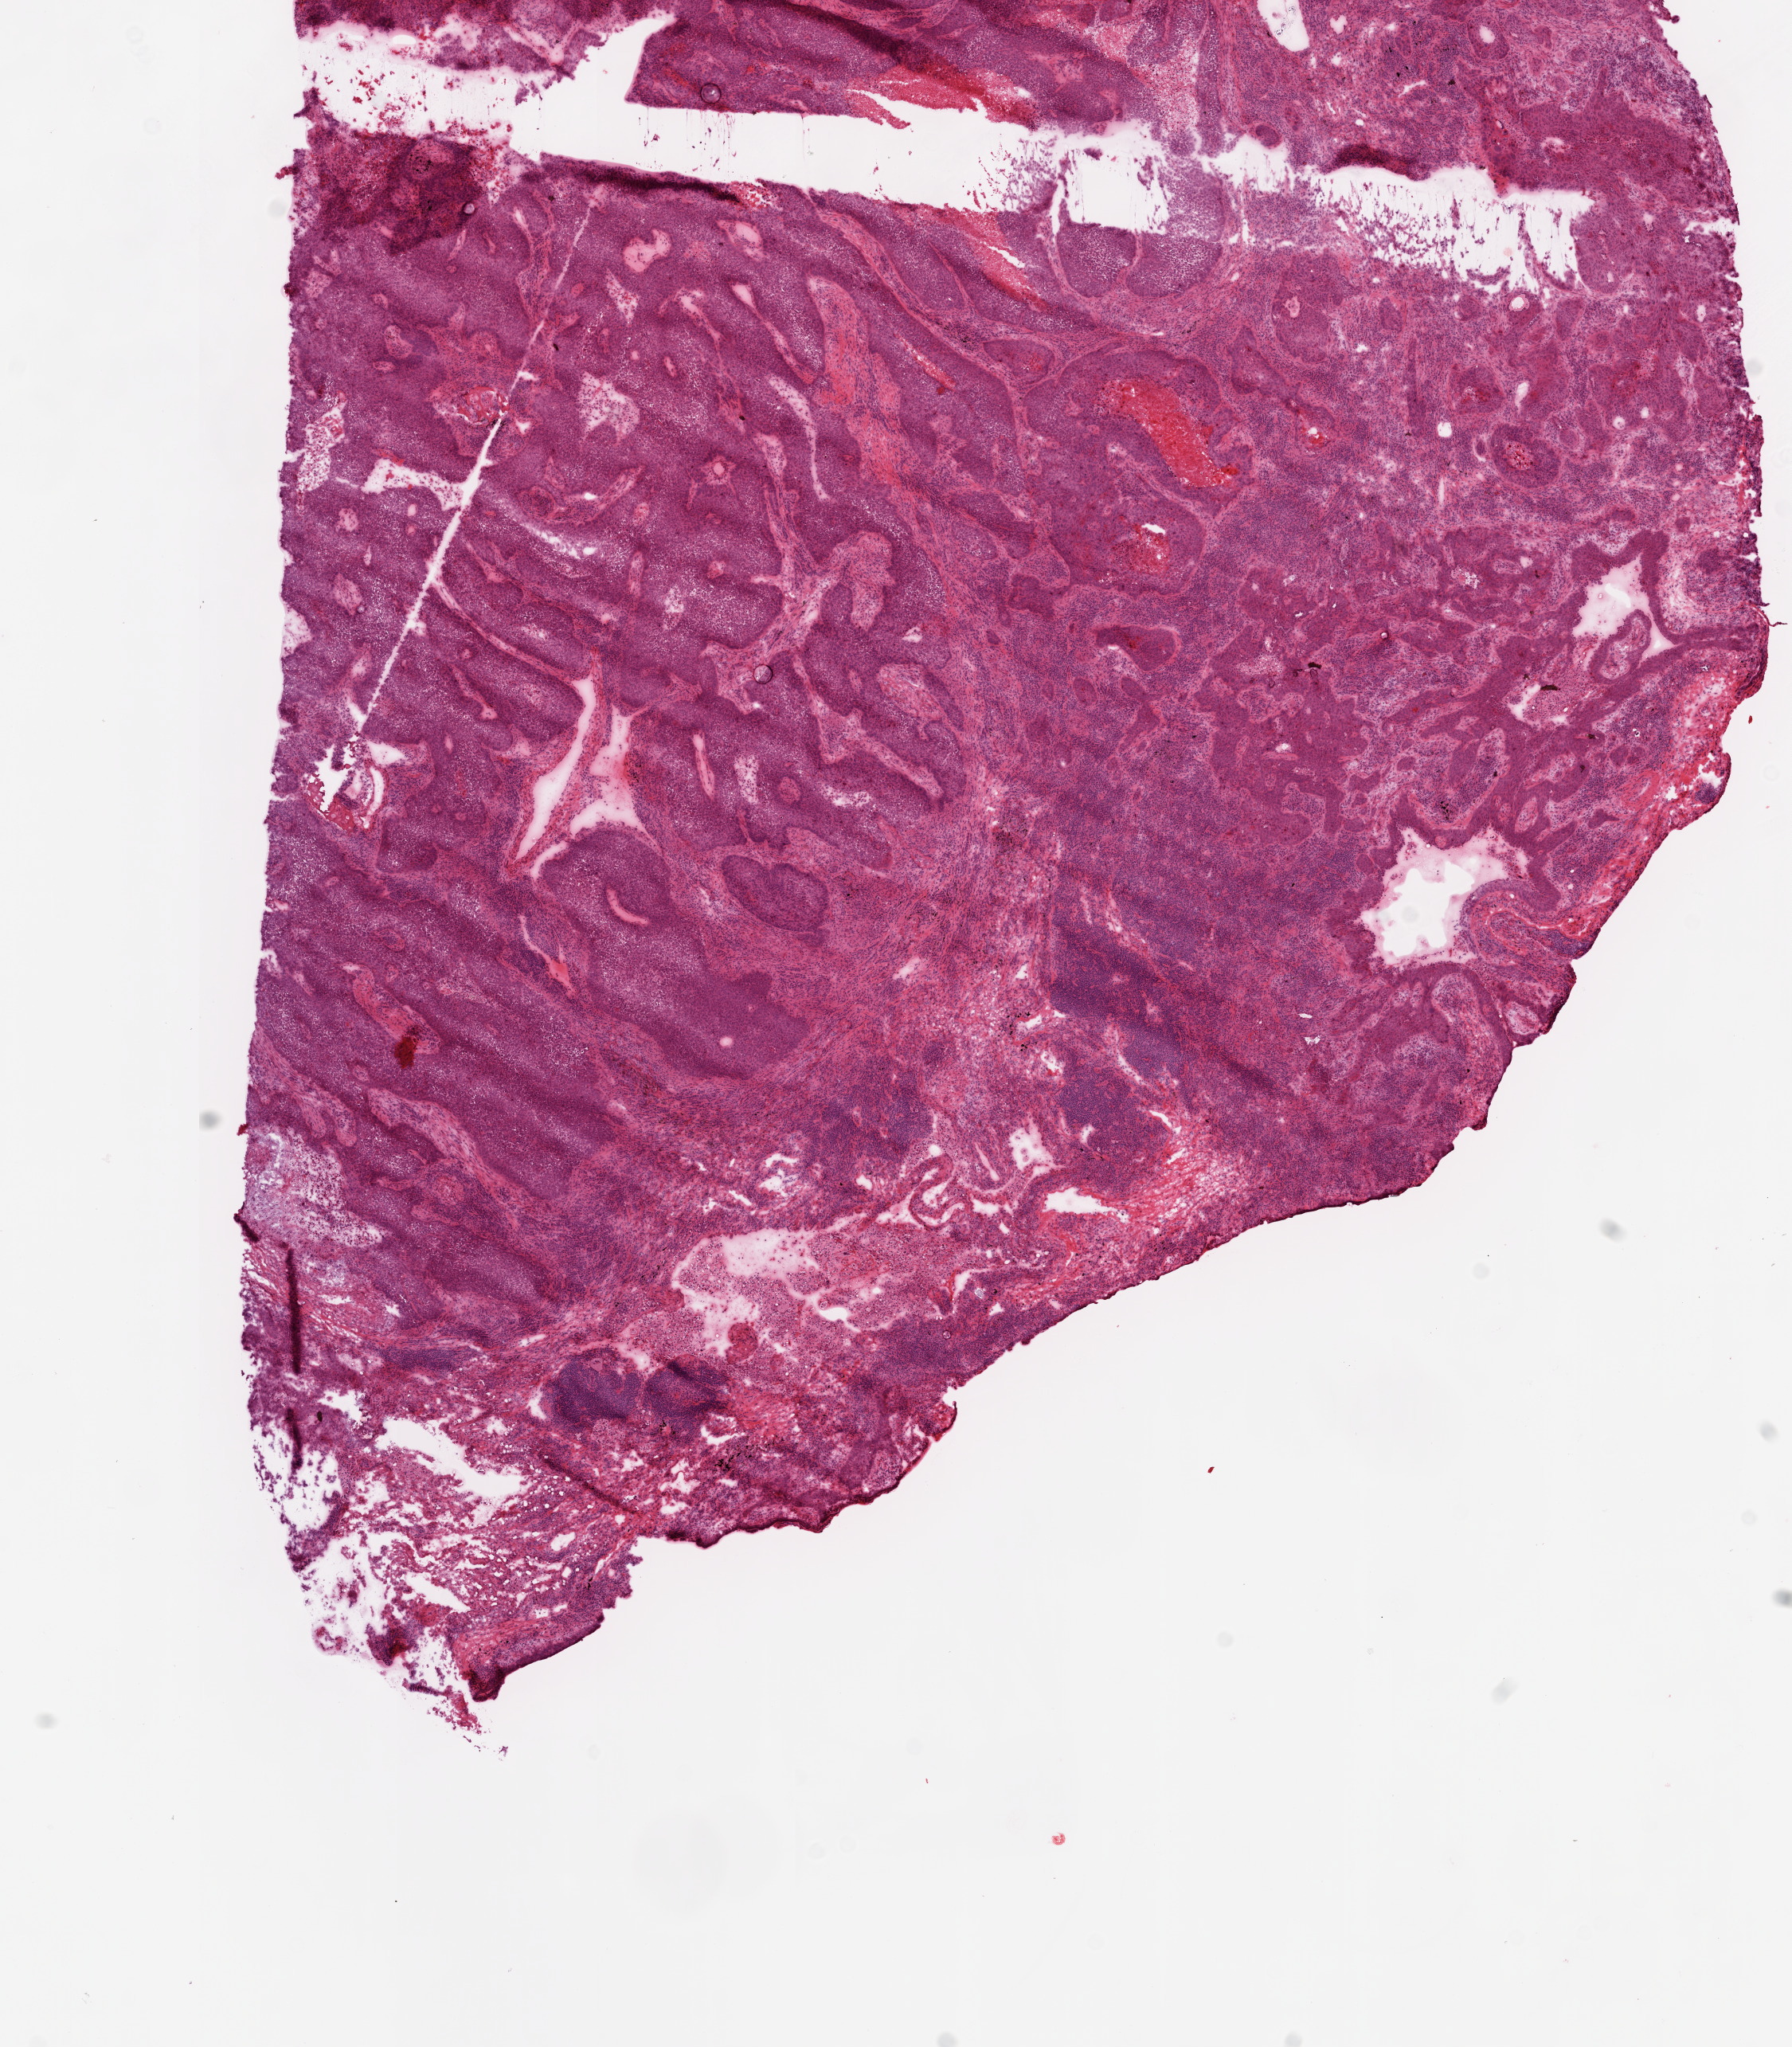
Whole-slide histology image, H&E-stained — shown as a low-resolution overview of the whole scanned area (about 9.0 x 10.3 mm, from a 20x scan); frozen section from the top of the tissue portion; sample: primary tumour, lung. Female, age 73 years at initial diagnosis. Slide review estimates, as recorded: tumour cells 75%, tumour nuclei 65%, normal cells 0%, stromal cells 15%, necrosis 10%.
• AJCC pathologic stage: IA
• pathologic diagnosis: Squamous cell carcinoma, NOS (upper lobe, lung)